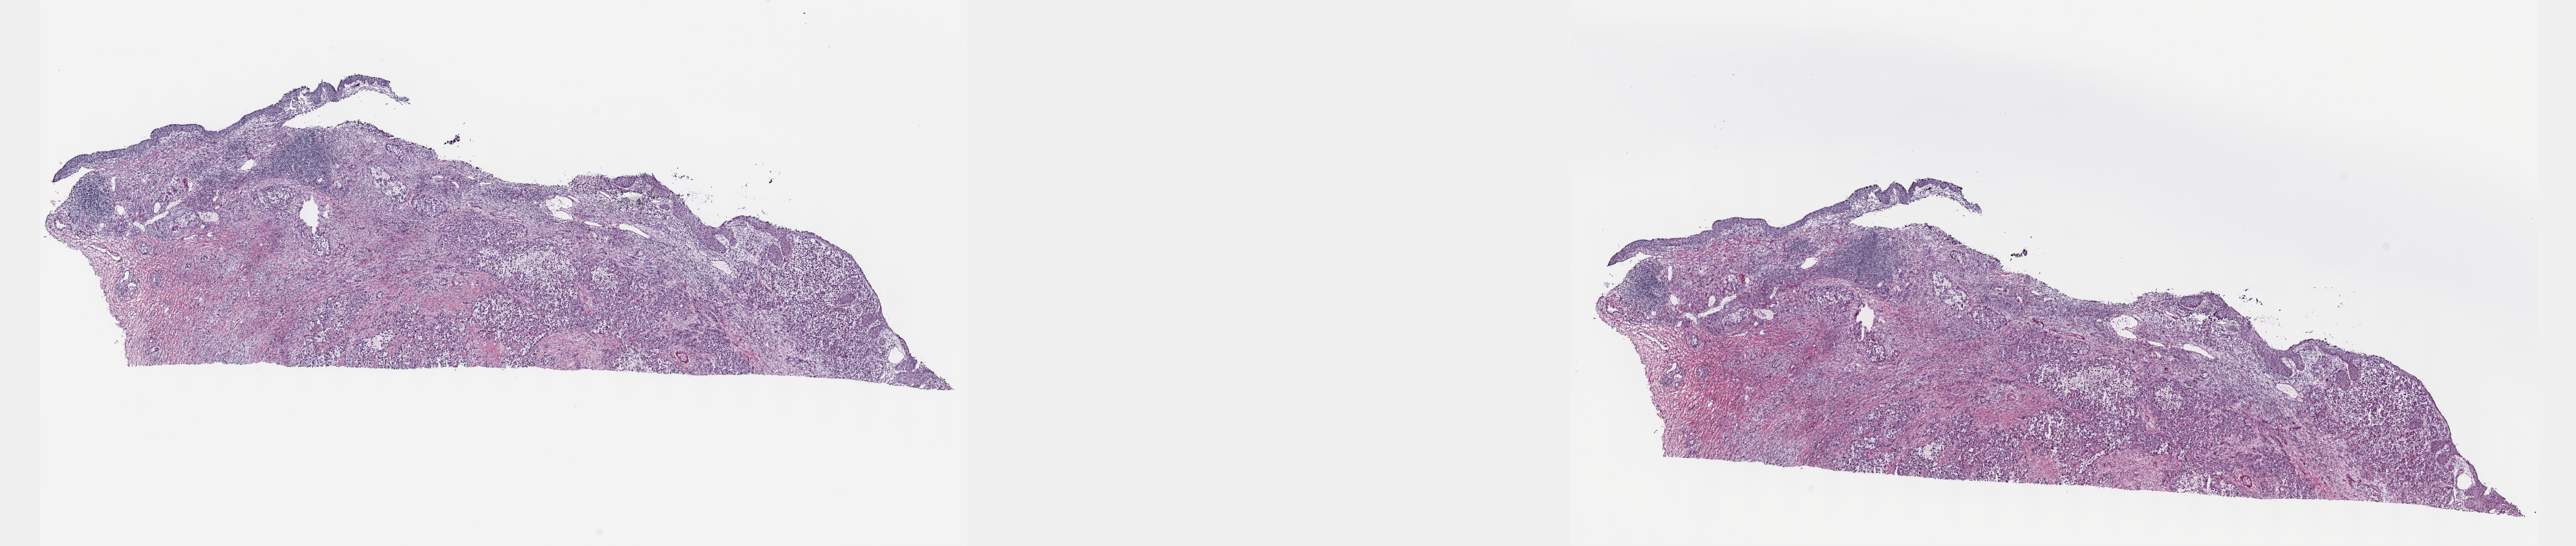
Whole-slide histology image, H&E, low-resolution overview of the scanned area, about 32.2 x 6.8 mm (from a 40x scan). Frozen section. Sample: primary tumour, bladder. Patient: female, age at initial diagnosis 79 years. Histologic grade: high grade. Pathologist review of this section (percent, as recorded): tumour cells 60%, tumour nuclei 70%, normal cells 10%, stromal cells 30%, necrosis 0%. Infiltration values recorded for this section: lymphocyte infiltration 30%, monocyte infiltration 70%, neutrophil infiltration 0%.
TNM: T2b N0. Diagnosis: Transitional cell carcinoma. AJCC pathologic stage: IV (5th edition). Lymph nodes positive (case pathology): 0 of 70 examined.